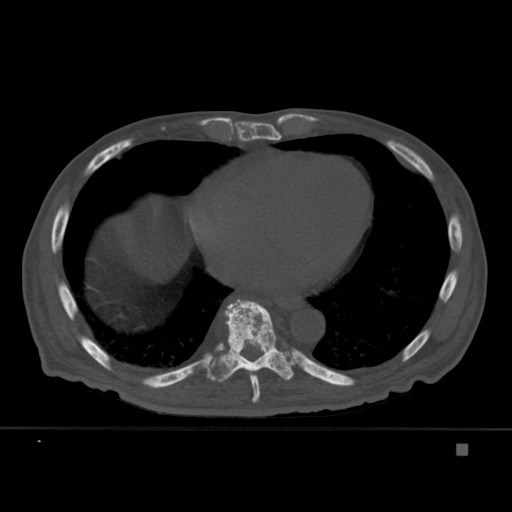
CT including the spine, one axial slice; bone window (W 1800 / L 400 HU); 1.5 mm slice thickness; 512 × 512 image matrix. Patient: male, 75 years. From the clinical record (not read from this slice): primary cancer: prostate.
Structures marked on this image (semi-automatically segmented with operator editing):
- T8 vertebra: box from (x=245, y=369) to (x=260, y=403) px
- T9 vertebra: (x=206, y=299)–(x=294, y=382)